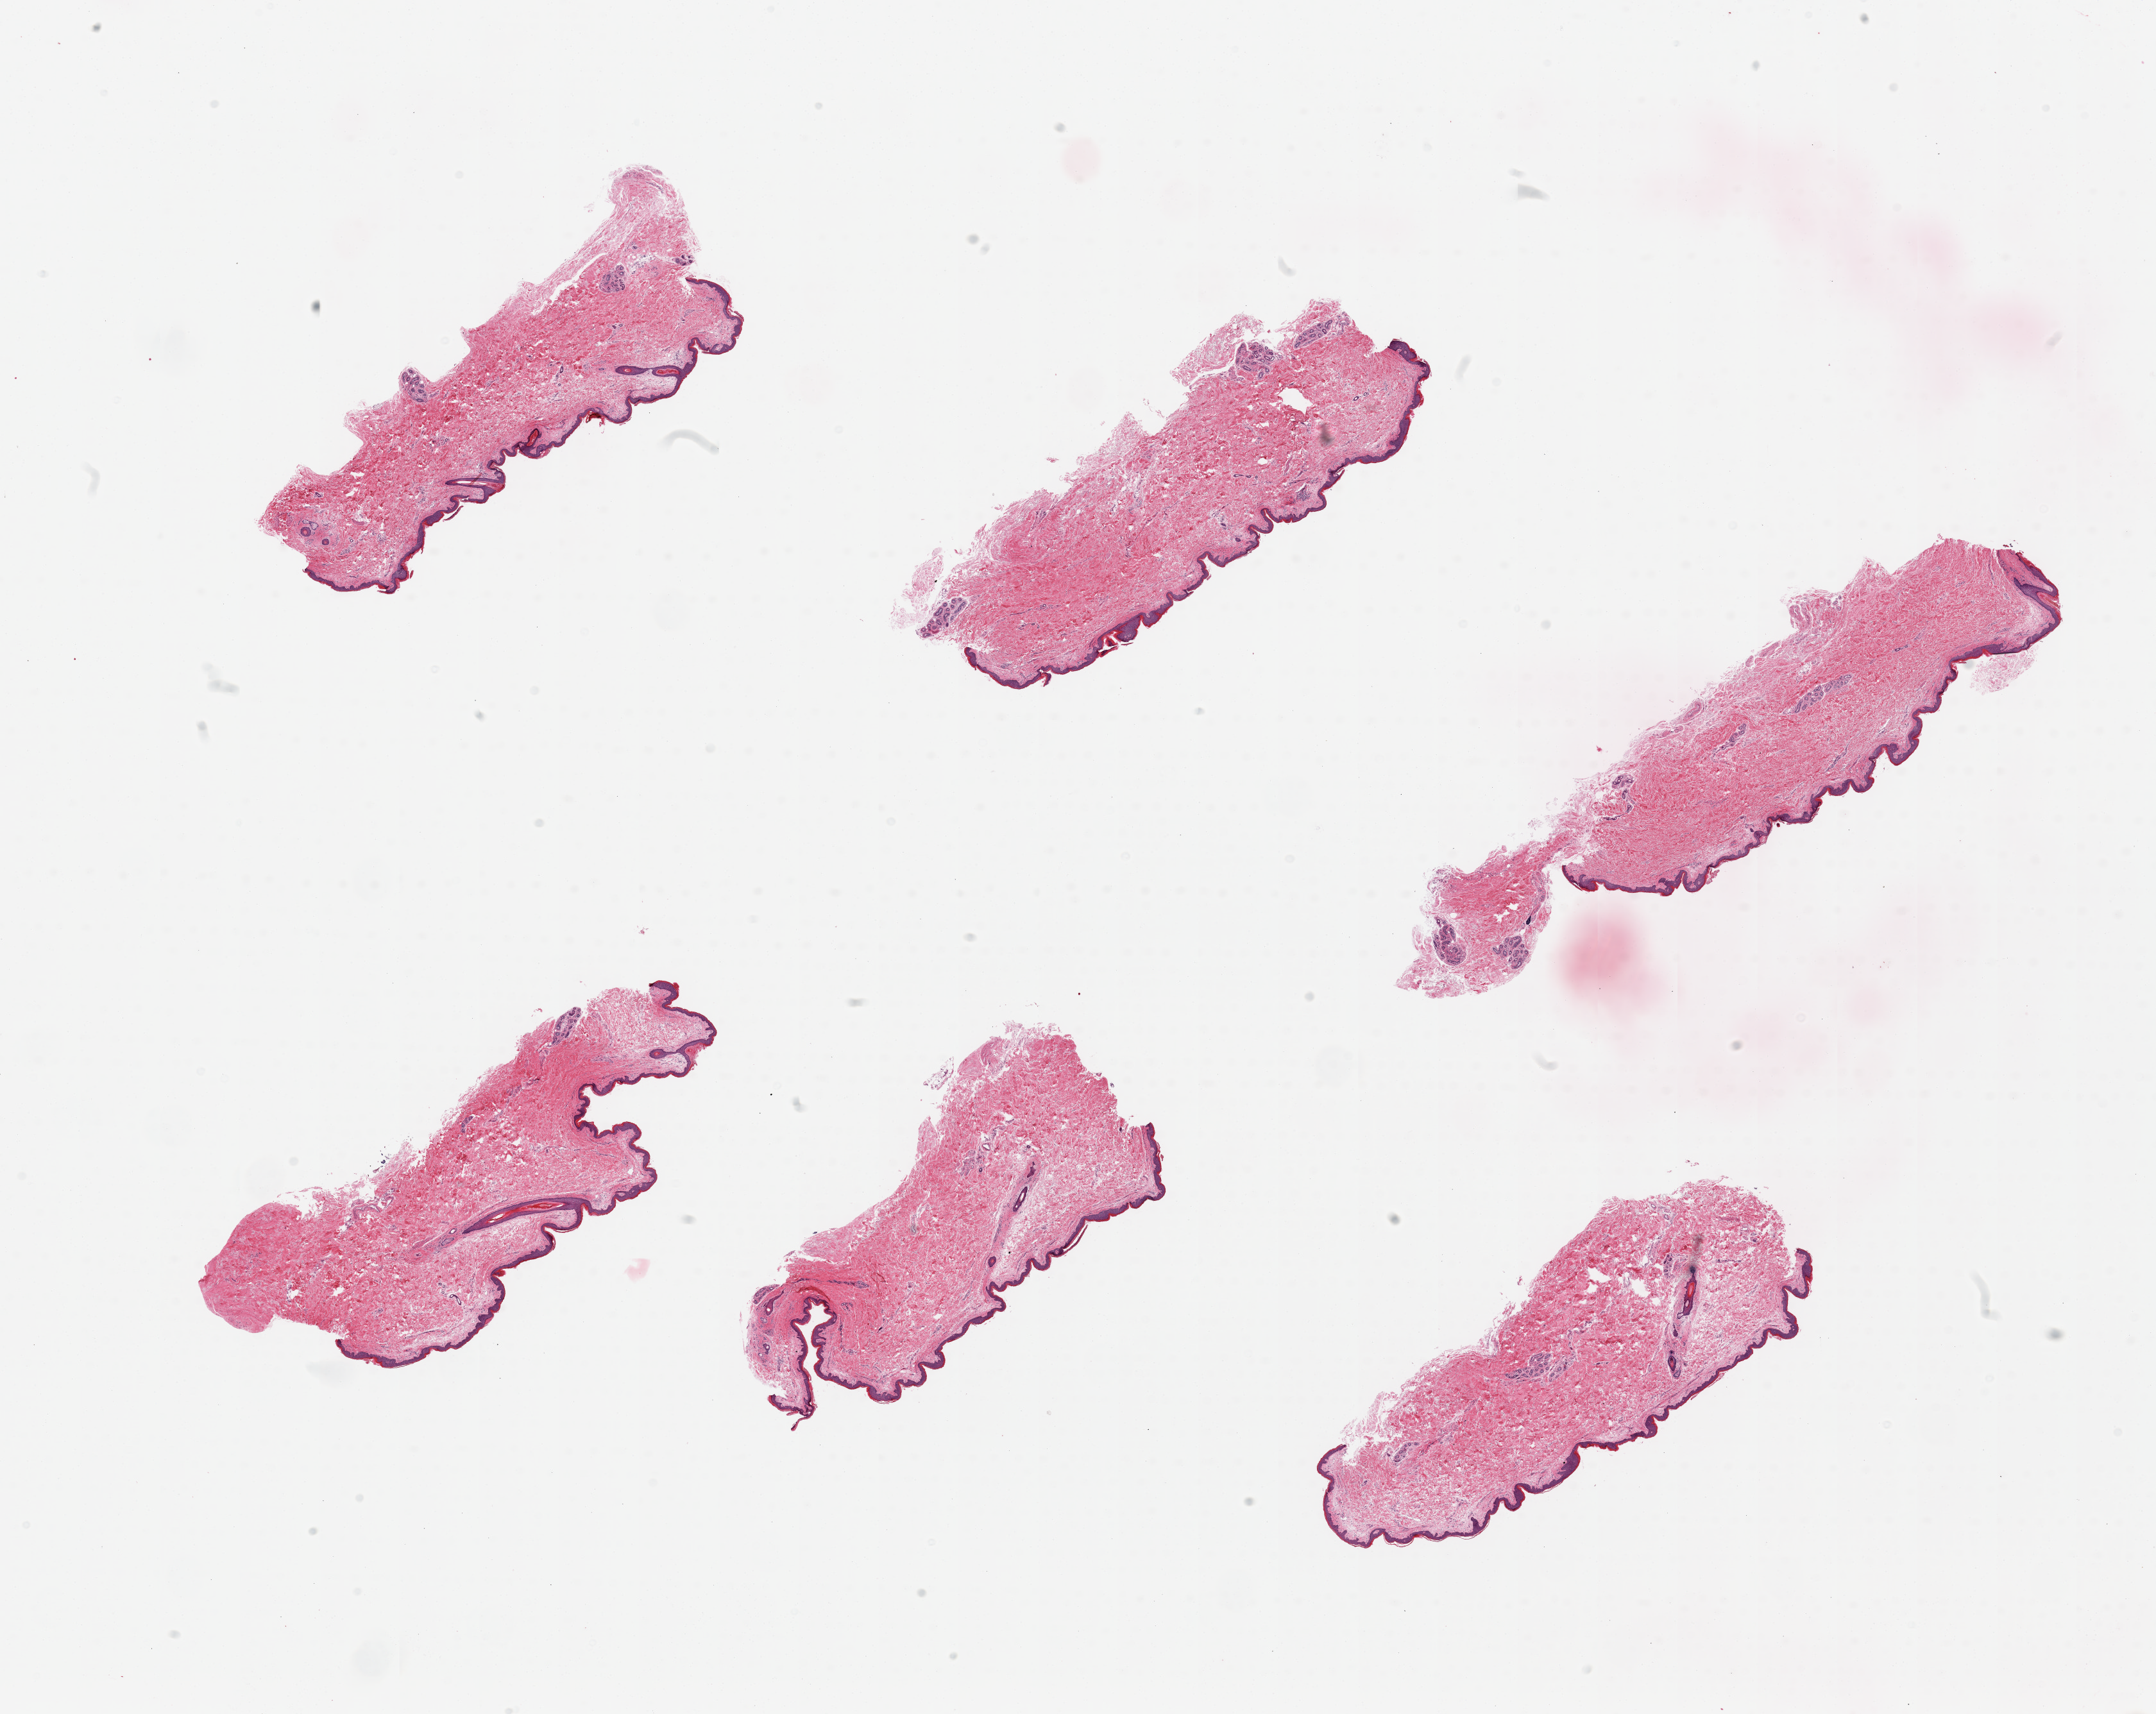
Digitized H&E-stained section, brightfield — low-resolution overview of the scanned area, about 26.6 x 21.1 mm; PAXgene-fixed, paraffin-embedded tissue; section of skin of suprapubic region (target tissue); donor tissue sample. Male donor.
Reviewer comment on this tissue sample: 2 pieces, minimal dermal fate; squamous epithelium is ~50-60 microns.